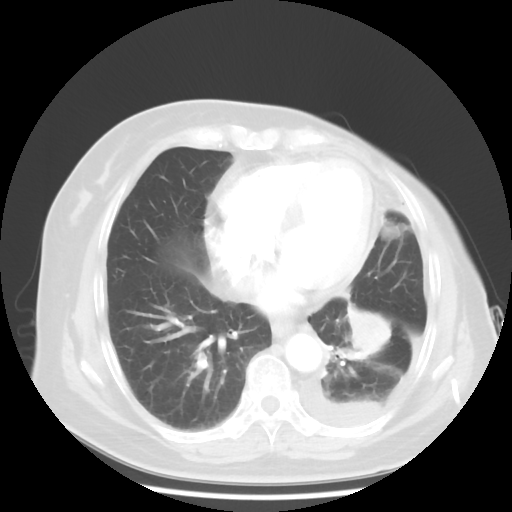
Chest CT, one axial slice; slice 16 of 48 in the series (ordered by position); reconstruction kernel STANDARD; 120 kVp; lung window (W 1500 / L -600 HU); 512 × 512 image matrix. Female patient, age 63 years. From the clinical record (not read from this slice): clinical TNM (as recorded): T2 N0 M1.
Annotated regions visible in this slice (bounding box drawn by a radiologist):
- lung tumour (recorded histology: adenocarcinoma): bounding box (x1, y1, x2, y2) in pixels: (338, 302, 413, 378)